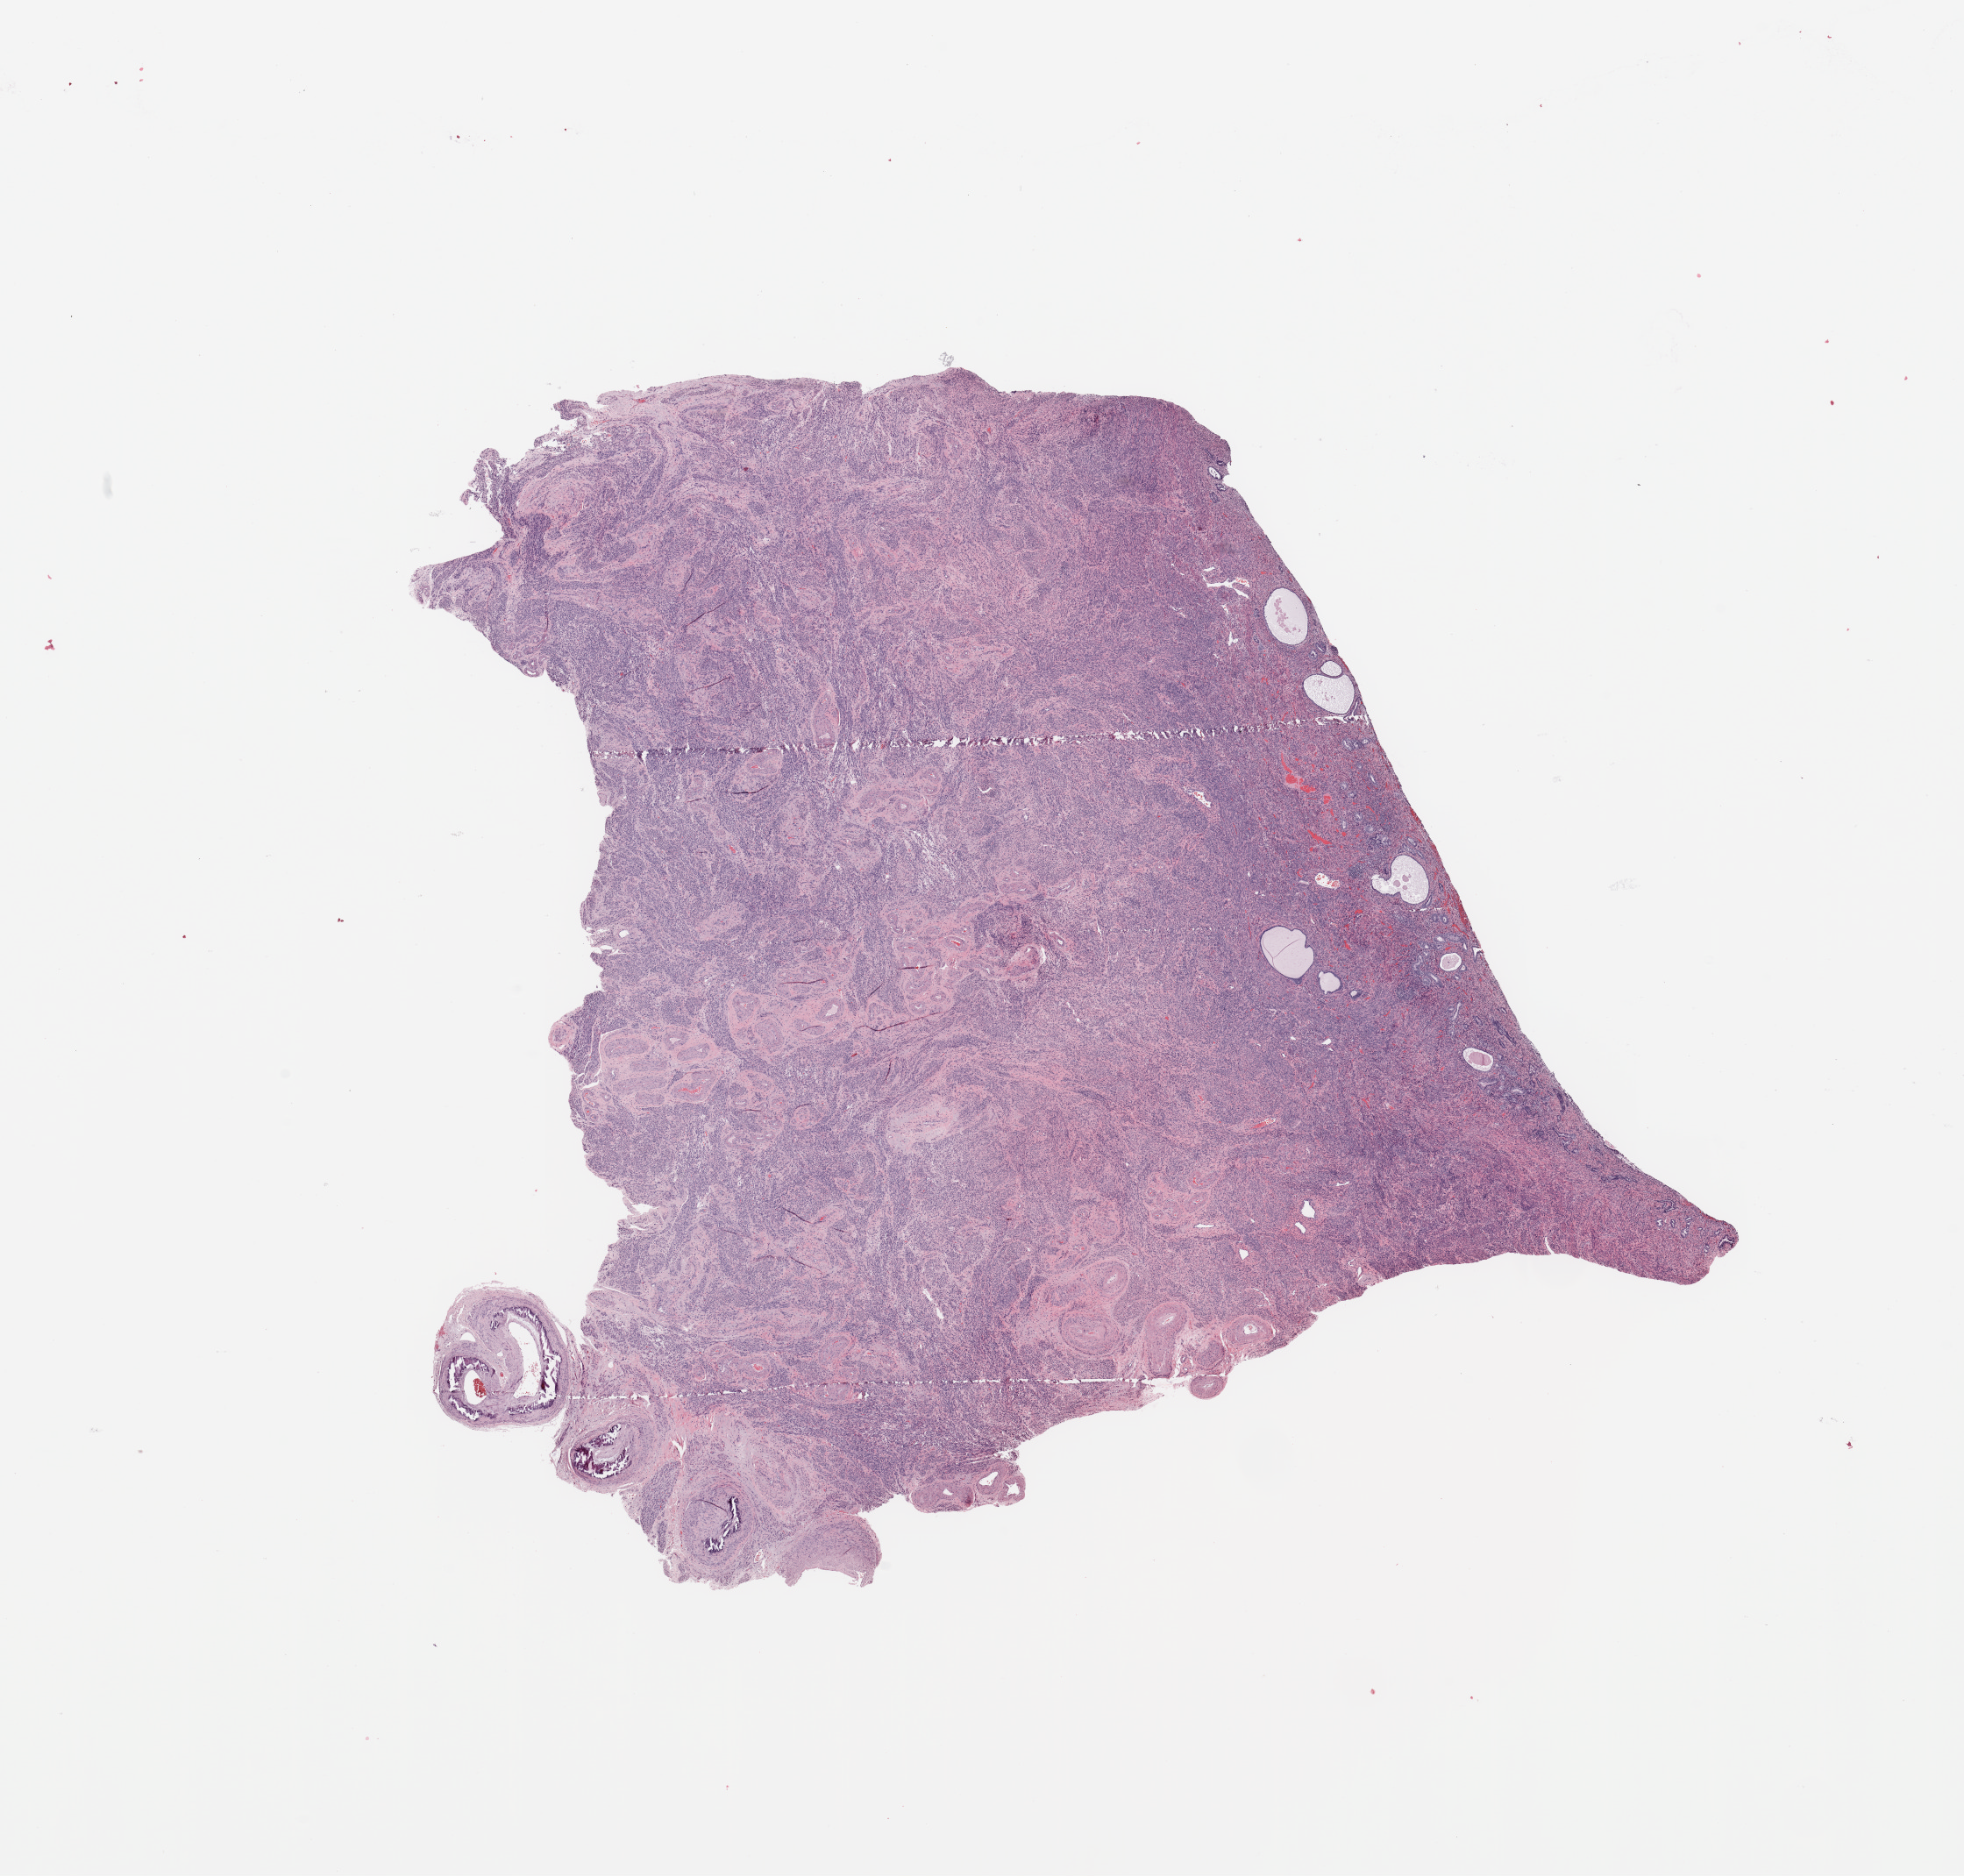
Digitized Hematoxylin and eosin (H&E) stained tissue section (whole slide), whole scanned area (about 17.7 x 16.9 mm, acquisition: 20x scan) shown as a low-resolution overview. Normal (non-tumour) tissue sample, uterus. Patient: female, age 81 years.
This section: normal (non-tumour) tissue from the same patient. Patient diagnosis: Endometrioid adenocarcinoma, NOS.